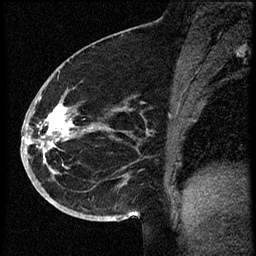
Breast MRI (dynamic contrast-enhanced), one sagittal slice. Dynamic contrast-enhanced study with each time point stored as its own series, time point 2 of 3 at this slice position (early post-contrast, ordered by acquisition time). 1.5 T. TE 4.2 ms, TR 18.9 ms. 2 mm slice thickness. 256 × 256 image matrix, field of view 200 × 200 mm. Female patient. Case-level facts recorded for this patient, not image findings: setting: breast cancer imaged before/during neoadjuvant chemotherapy; receptor status: HR-positive, HER2-negative.
Annotated regions visible in this slice (semi-automatic segmentation, software-assisted and operator-edited):
- analysis volume of interest (the breast-tissue region the enhancement analysis was run in; not a lesion): box from (x=30, y=87) to (x=114, y=173) px
- tumour enhancement mask (voxels above the 100 % enhancement threshold inside the analysis volume of interest): (x=30, y=104)–(x=74, y=155)